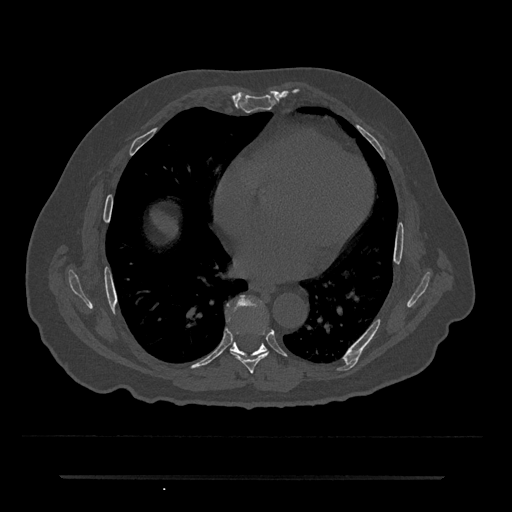
CT including the spine, one axial slice. Slice 363 of 797 in the series (ordered by position). Reconstruction kernel Br40s/3. 120 kVp. Bone window (W 1800 / L 400 HU). 0.5 mm slice thickness. 512 × 512 image matrix, field of view 437 × 437 mm. Male patient, age 69 years. From the clinical record (not read from this slice): primary cancer: prostate.
Annotated regions visible in this slice (semi-automatic segmentation, software-assisted and operator-edited):
- T7 vertebra: box from (x=231, y=331) to (x=269, y=373) px
- T8 vertebra: (x=227, y=297)–(x=267, y=356)